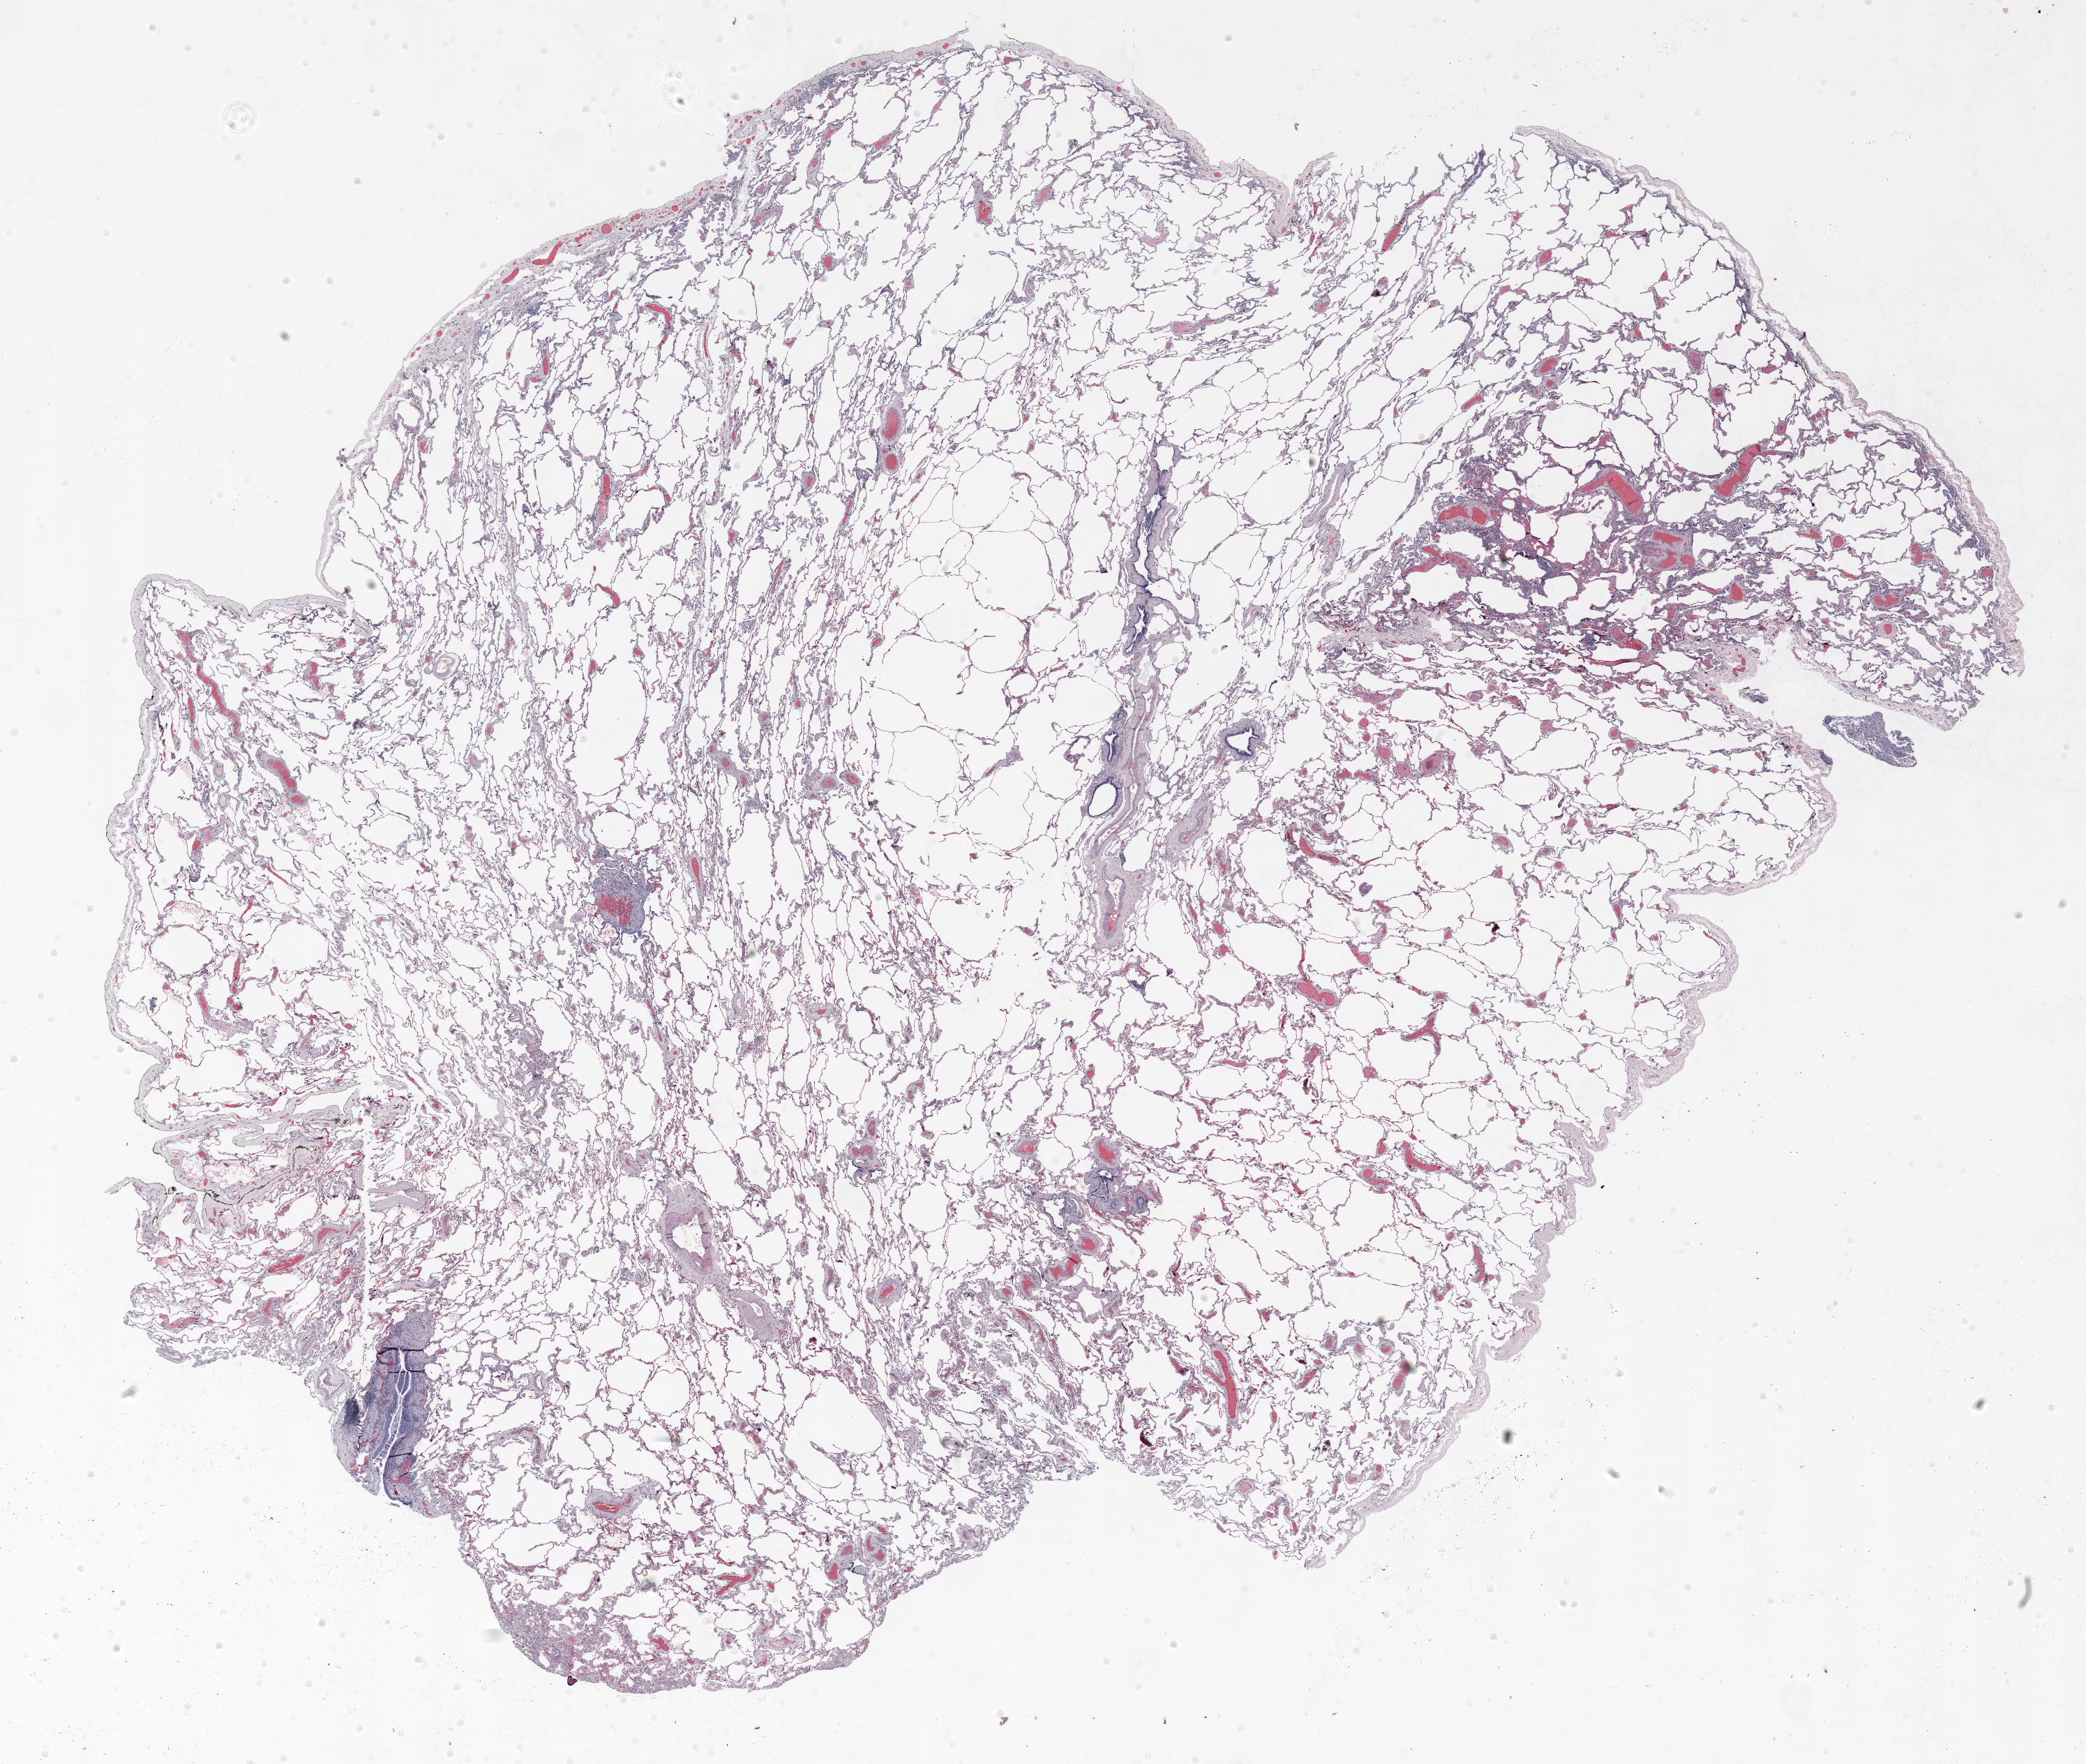
H&E-stained whole-slide image, shown as a low-resolution overview of the whole scanned area (about 24.0 x 20.3 mm, from a 20x scan). Formalin-fixed paraffin-embedded (FFPE) section. Lung tissue. Female, age 66 at enrolment. Former smoker at enrolment. Grade: moderately differentiated (G2).
* stage (AJCC 6th edition): IA
* tumour size (pathology): 11 mm
* primary tumour location (clinical record): right middle lobe
* participant's lung-cancer diagnosis: Adenocarcinoma, NOS (ICD-O-3 8140/3)